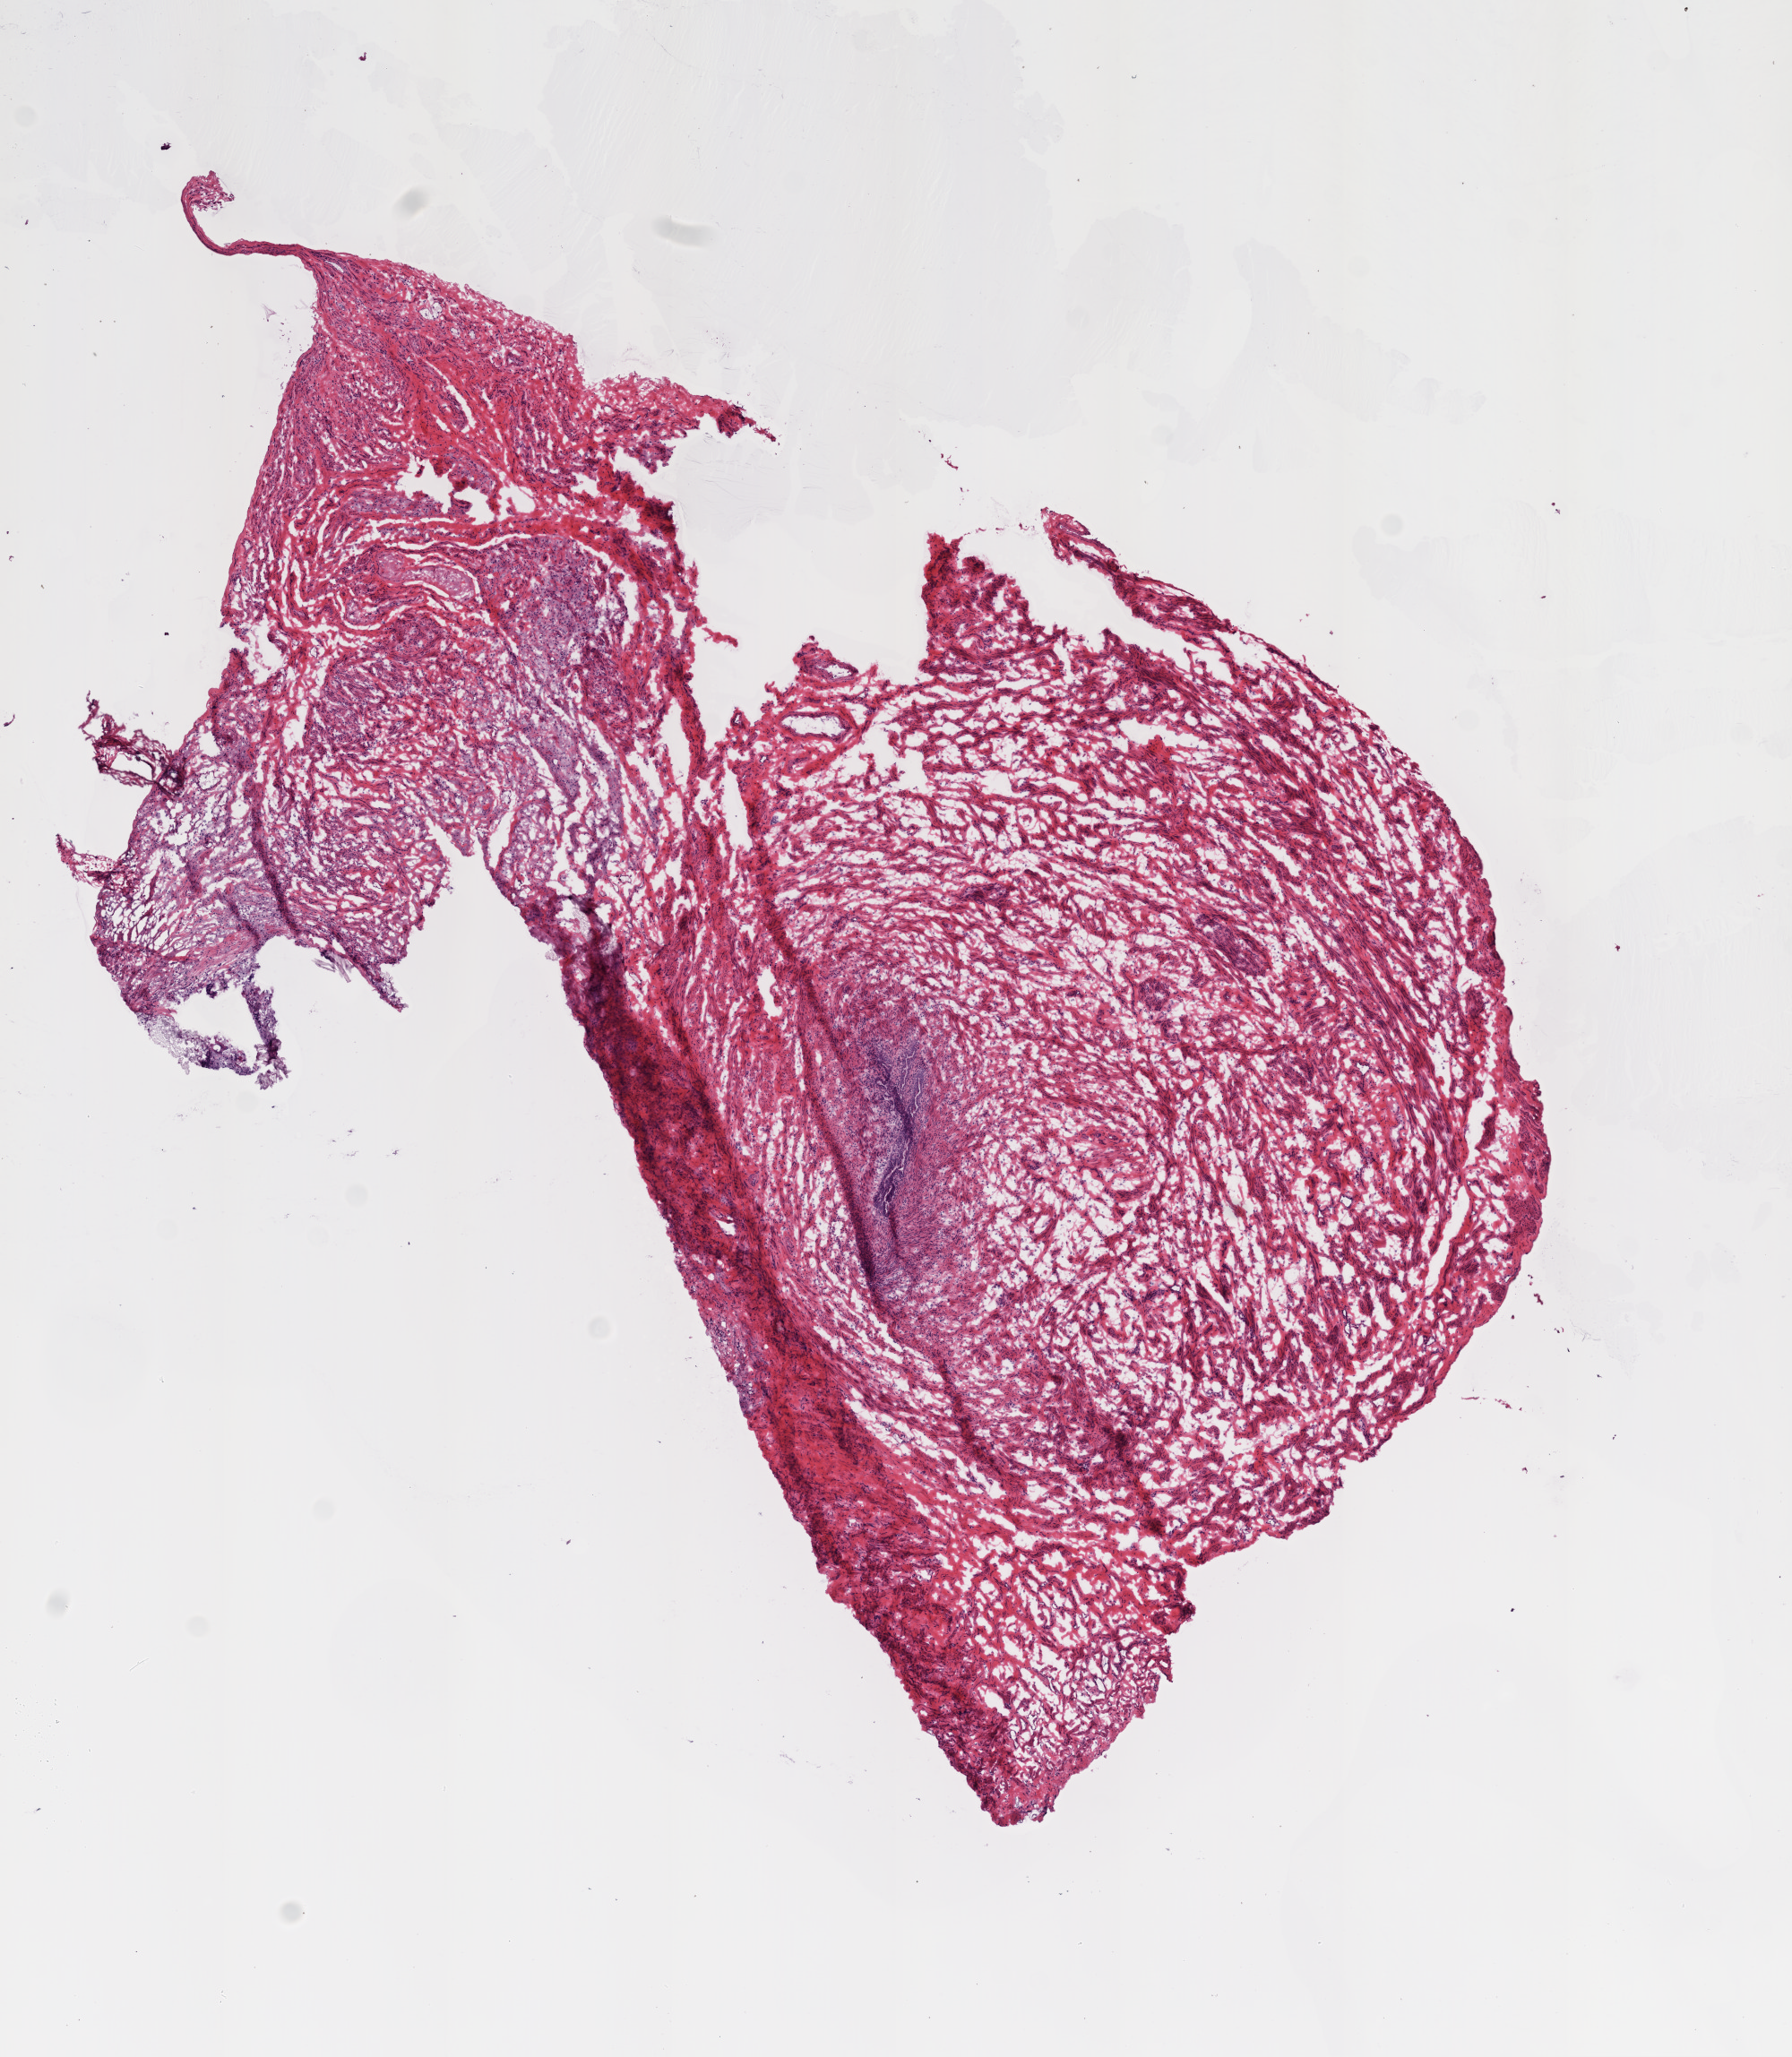
Hematoxylin and eosin (H&E) stained whole-slide image — shown as a low-resolution overview of the whole scanned area (about 8.0 x 9.2 mm, acquisition: 20x scan); frozen section from the bottom of the tissue portion; ovary, solid tissue normal (non-tumour tissue) sample. Female patient; age at initial diagnosis 56 years.
* this section: solid tissue normal sample (biorepository sample class)
* patient diagnosis: Serous cystadenocarcinoma, NOS